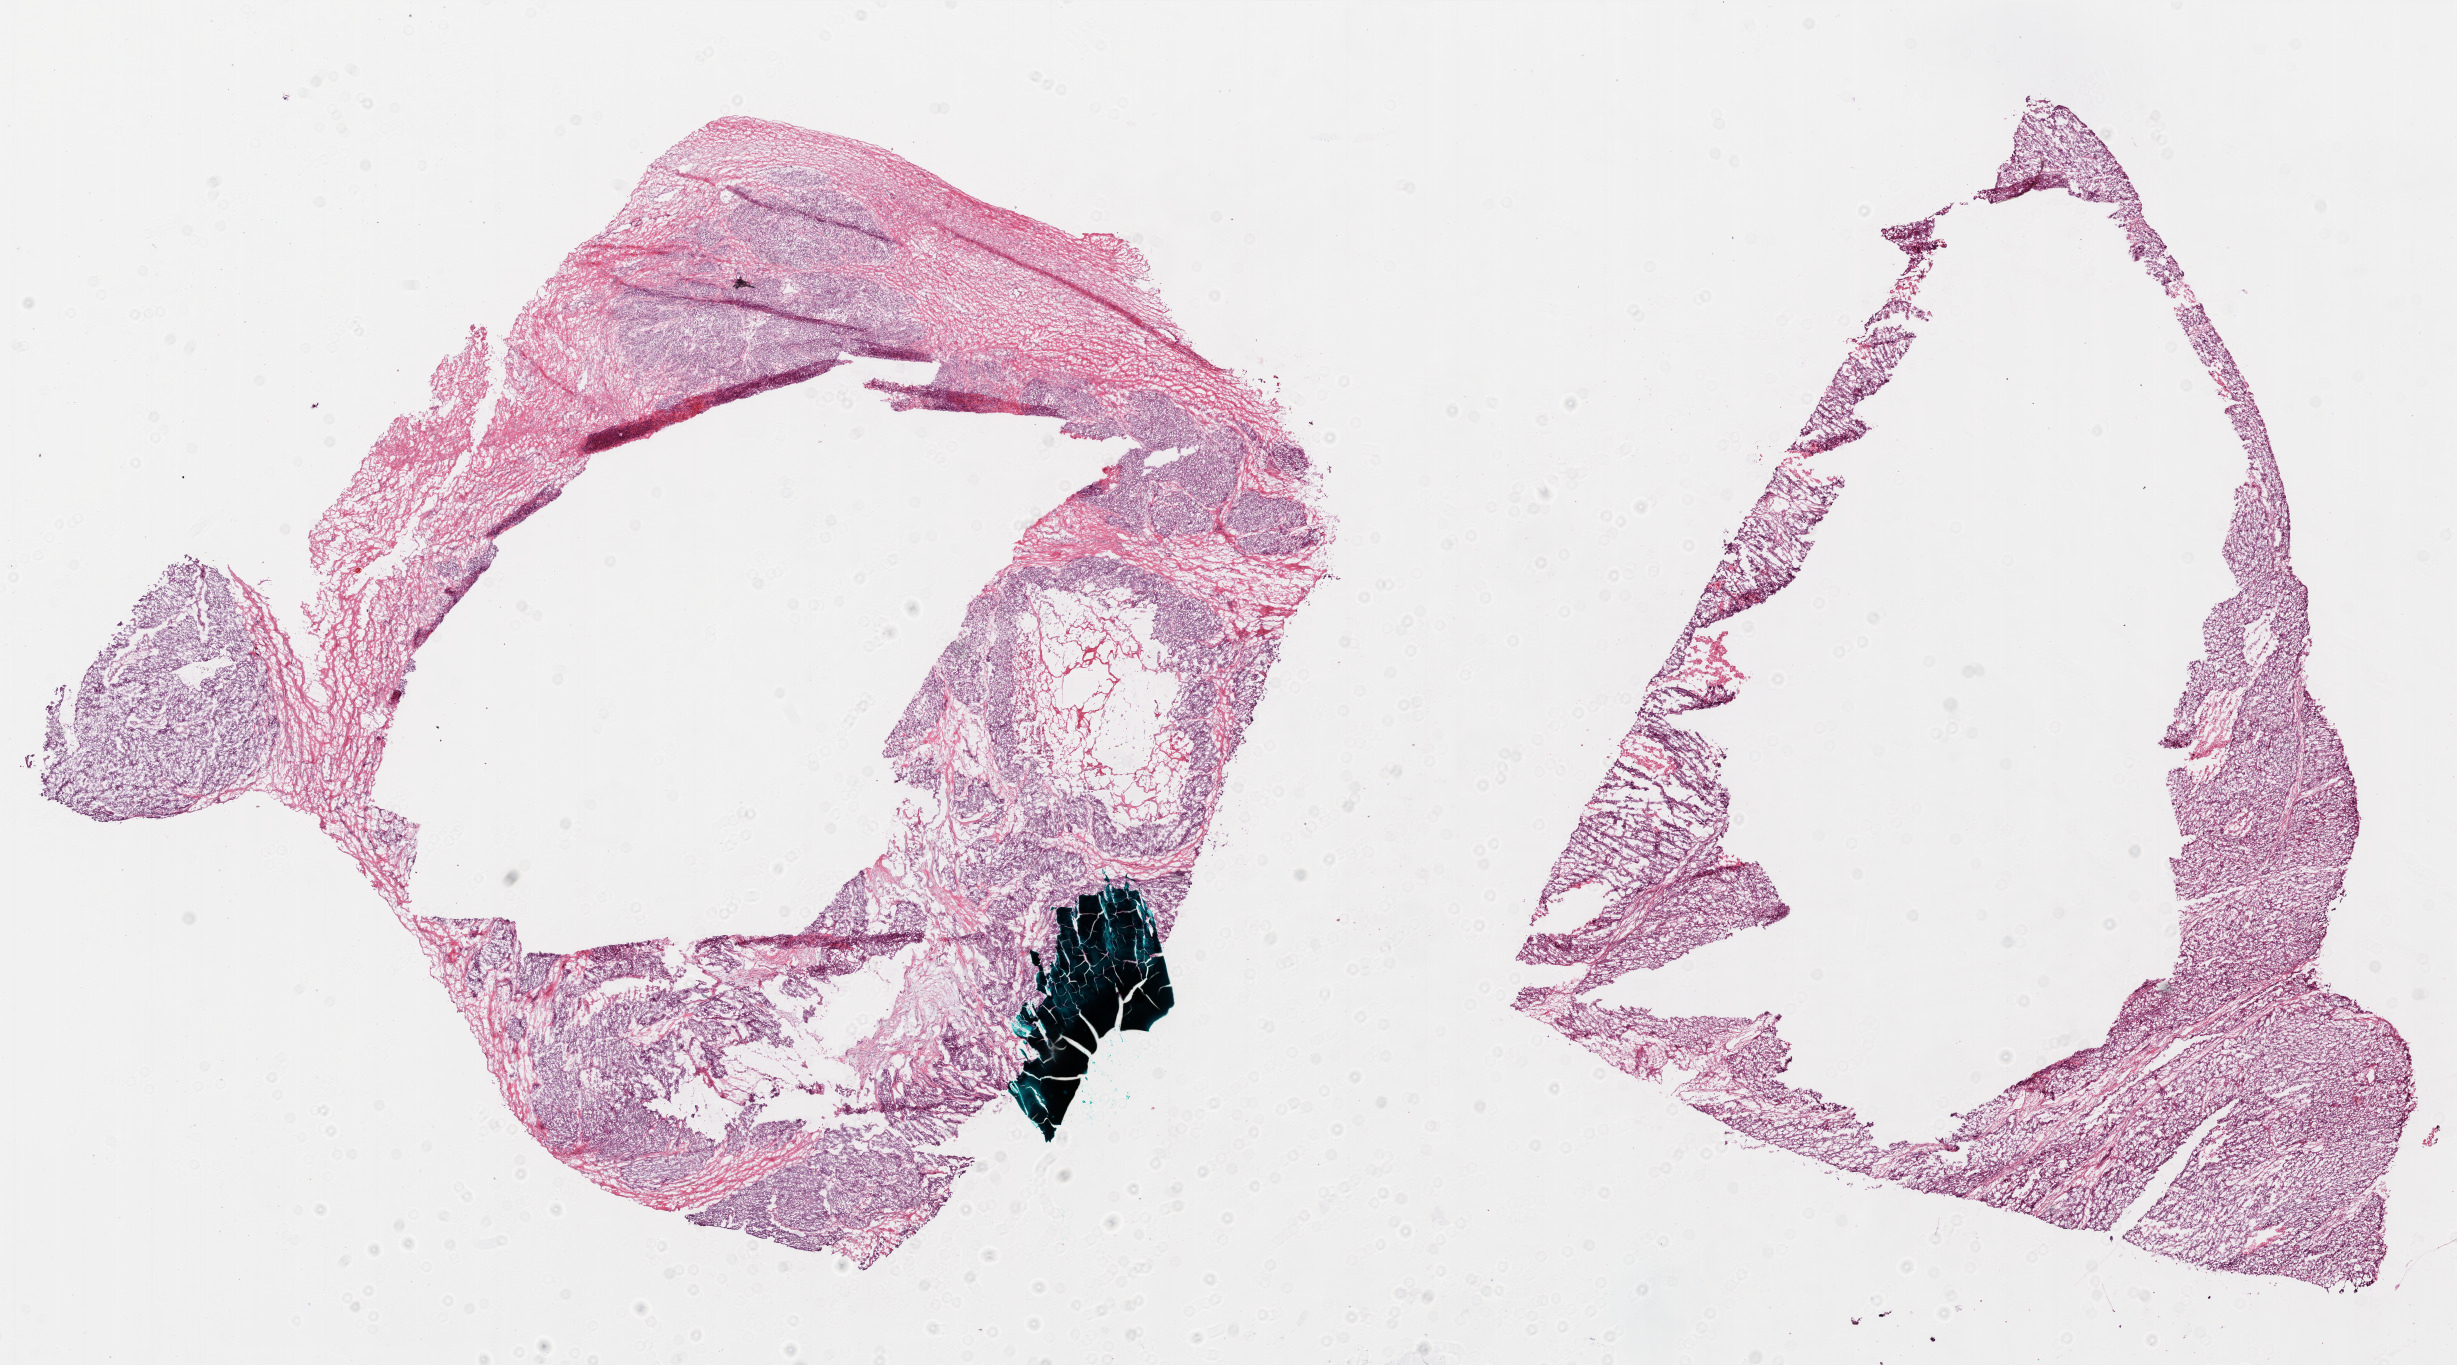
Digitized Hematoxylin and eosin (H&E) stained tissue section (whole slide), whole scanned area (about 19.8 x 11.0 mm, slide scanned at 20x) shown as a low-resolution overview. Frozen section from the bottom of the tissue portion. Sample: primary tumour, ovary. Female patient; age at initial diagnosis 58 years. Histologic grade: G3 (poorly differentiated). Slide review estimates, as recorded: tumour cells 50%, tumour nuclei 85%, normal cells 0%, stromal cells 50%, necrosis 0%.
FIGO stage: IIIC. Diagnosis: Serous cystadenocarcinoma, NOS. Laterality: bilateral.